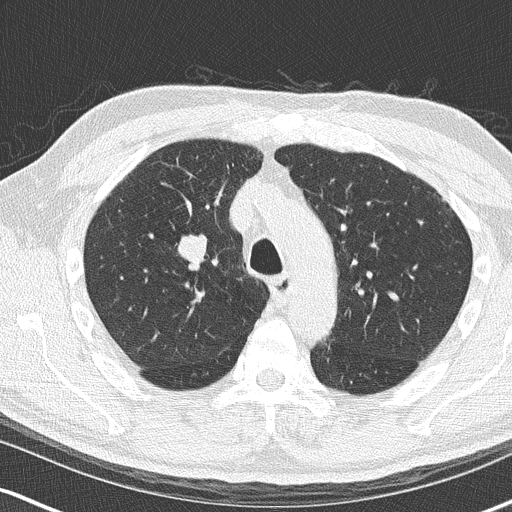
Chest CT (low-dose screening protocol), one axial image, second annual screen, lung window (W 1500 / L -600 HU), 120 kVp, 512 × 512 image matrix, field of view 320 × 320 mm. Male, age 68 years at enrolment. Current smoker at enrolment.
Expert reader's lesion annotation, bounding box <152,224,217,287> (left, top, right, bottom; pixels). Screening reader's record for this exam (one nodule recorded; not confirmed to be the boxed lesion): non-calcified nodule or mass ≥4 mm, right upper lobe, 18 × 15 mm, smooth margins, soft tissue attenuation, pre-existing on the prior screen: no. Official screen result: positive, change unspecified: nodule(s) >= 4 mm or enlarging nodule(s), mass(es), or other non-specific abnormalities suspicious for lung cancer. Later outcome: lung cancer diagnosed 136 days after this screen — small cell carcinoma, NOS, right upper lobe, stage IIIB (AJCC 6th edition), 20 mm at pathology.